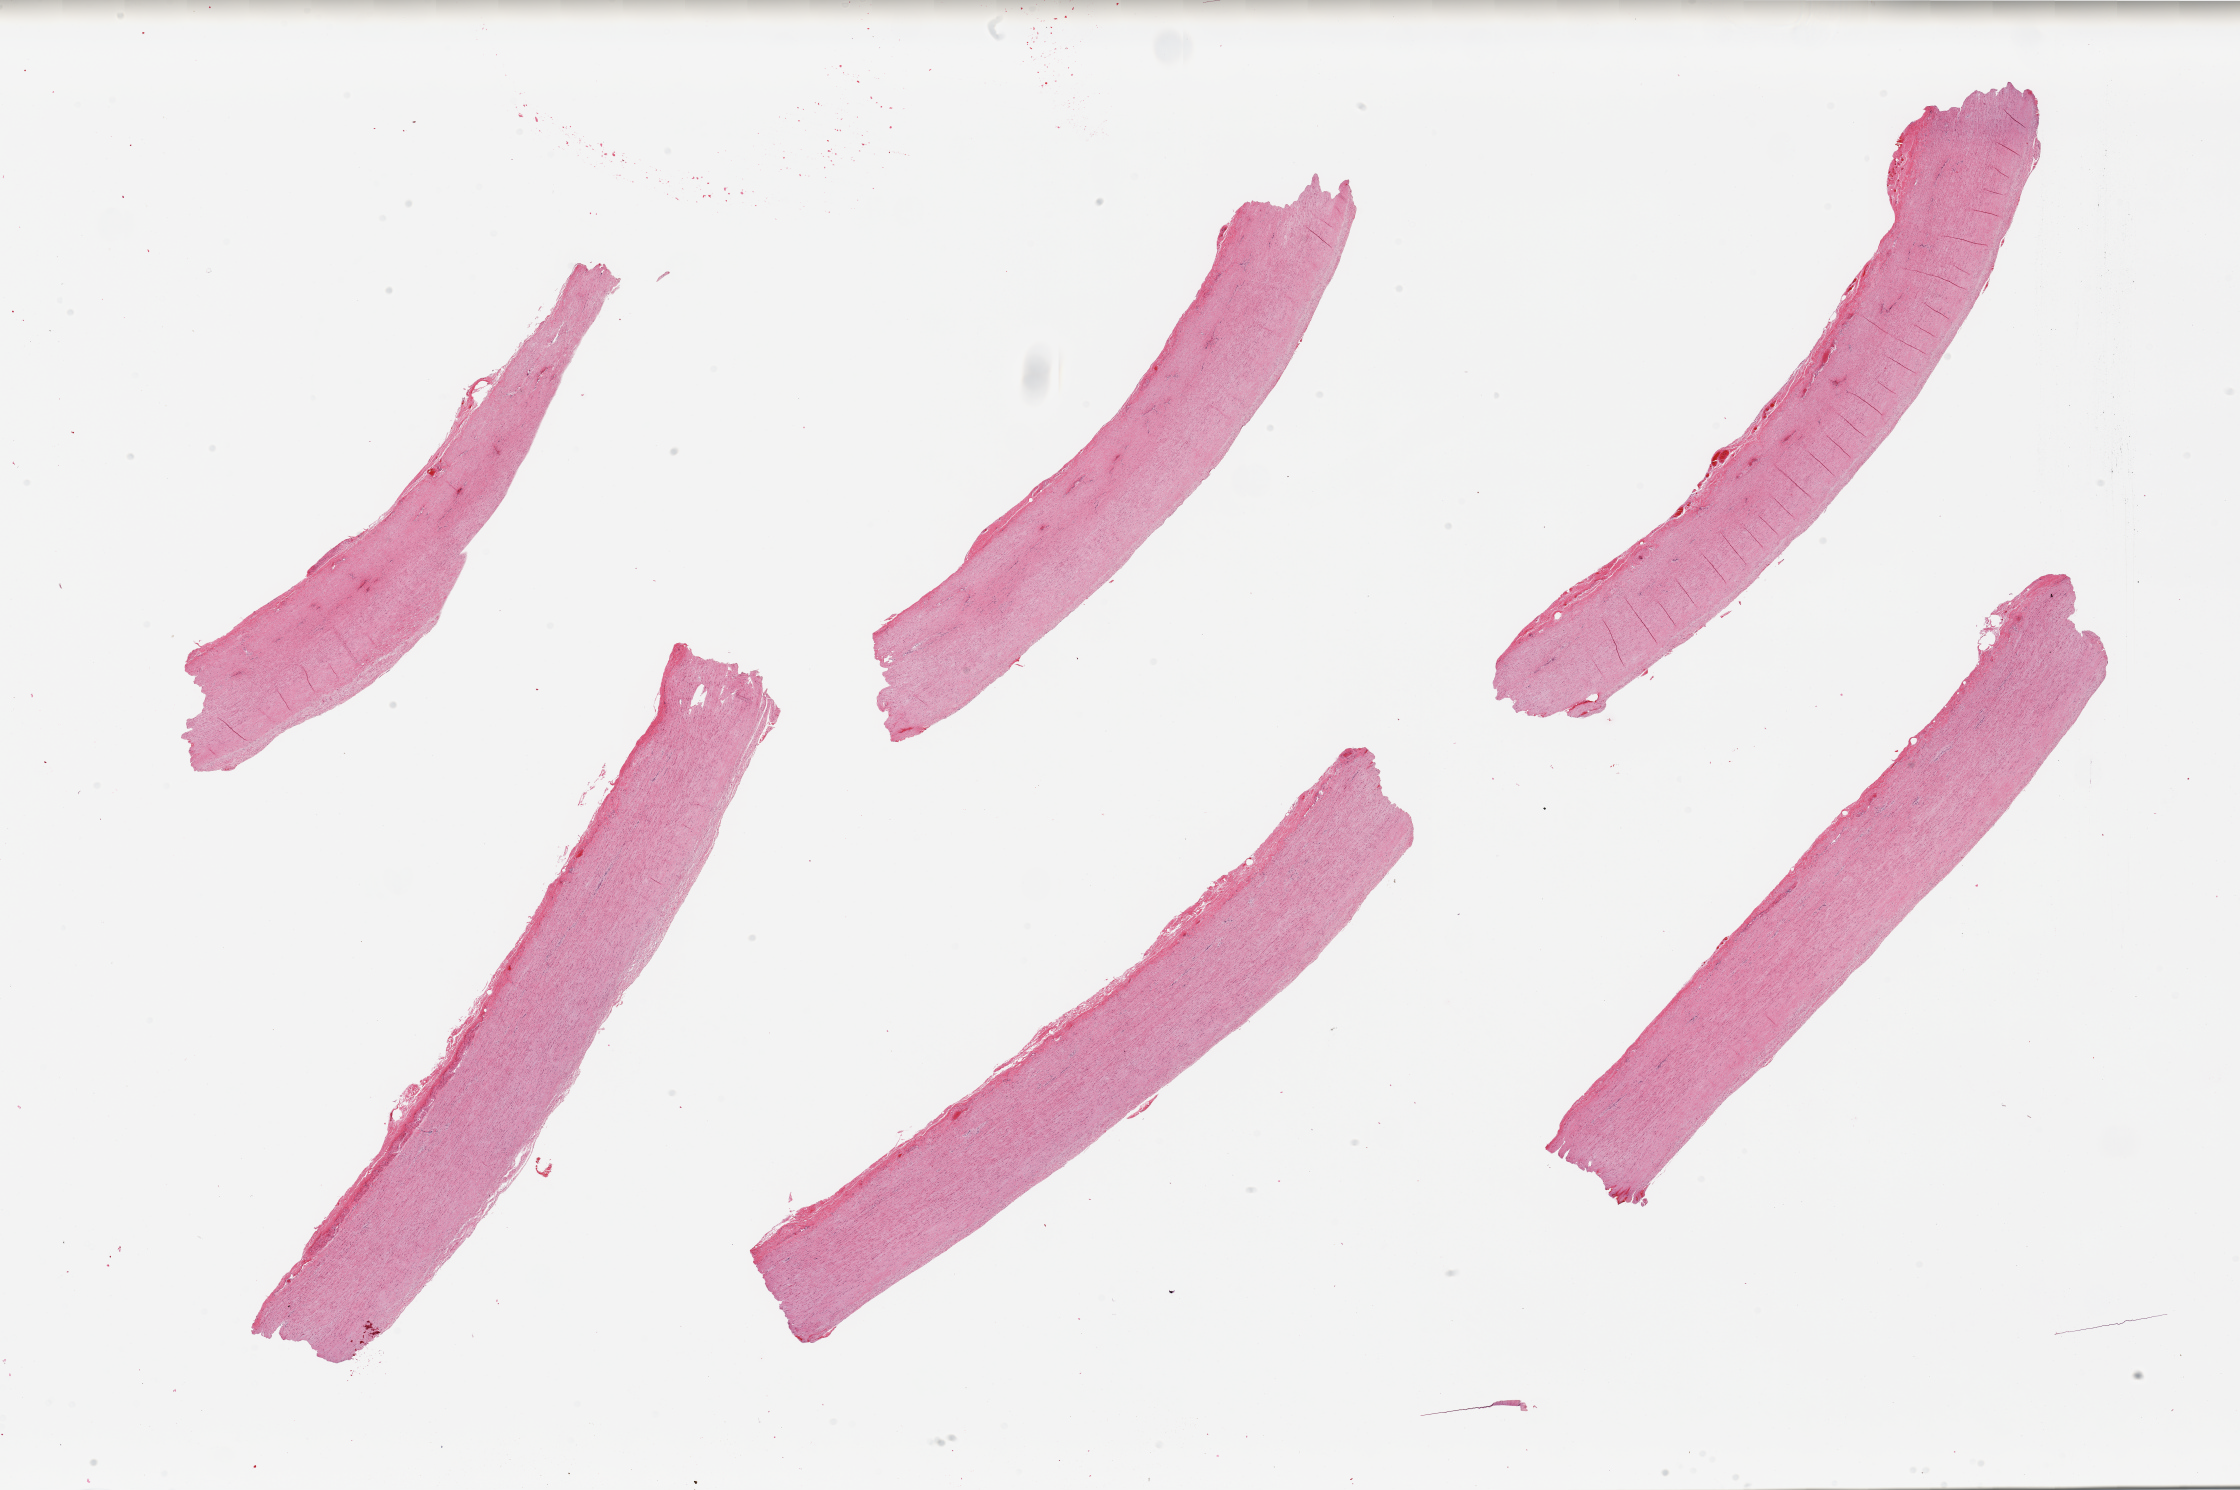
Whole-slide image, haematoxylin and eosin stain, brightfield — whole scanned area (about 35.4 x 23.6 mm) shown as a low-resolution overview, PAXgene-fixed, paraffin-embedded tissue, sampled site (target tissue): aorta, tissue donor sample. Donor sex: male.
Pathologist's review note for this sample: 6 pieces; moderate medial degeneration.